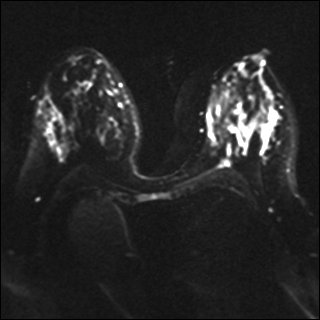
Breast MRI, one axial slice. Position 19 of 37 along the scan axis. Diffusion-weighted series; image 2 of 4 stored at this slice position (different b-values; order by instance number). 1.5 T. 4 mm slice thickness. 320 × 320 image matrix, field of view 340 × 340 mm. Female patient.
Structures marked on this image (expert manual segmentation):
- tumour on diffusion-weighted imaging: bounding box <237,125,251,142> (left, top, right, bottom; pixels)